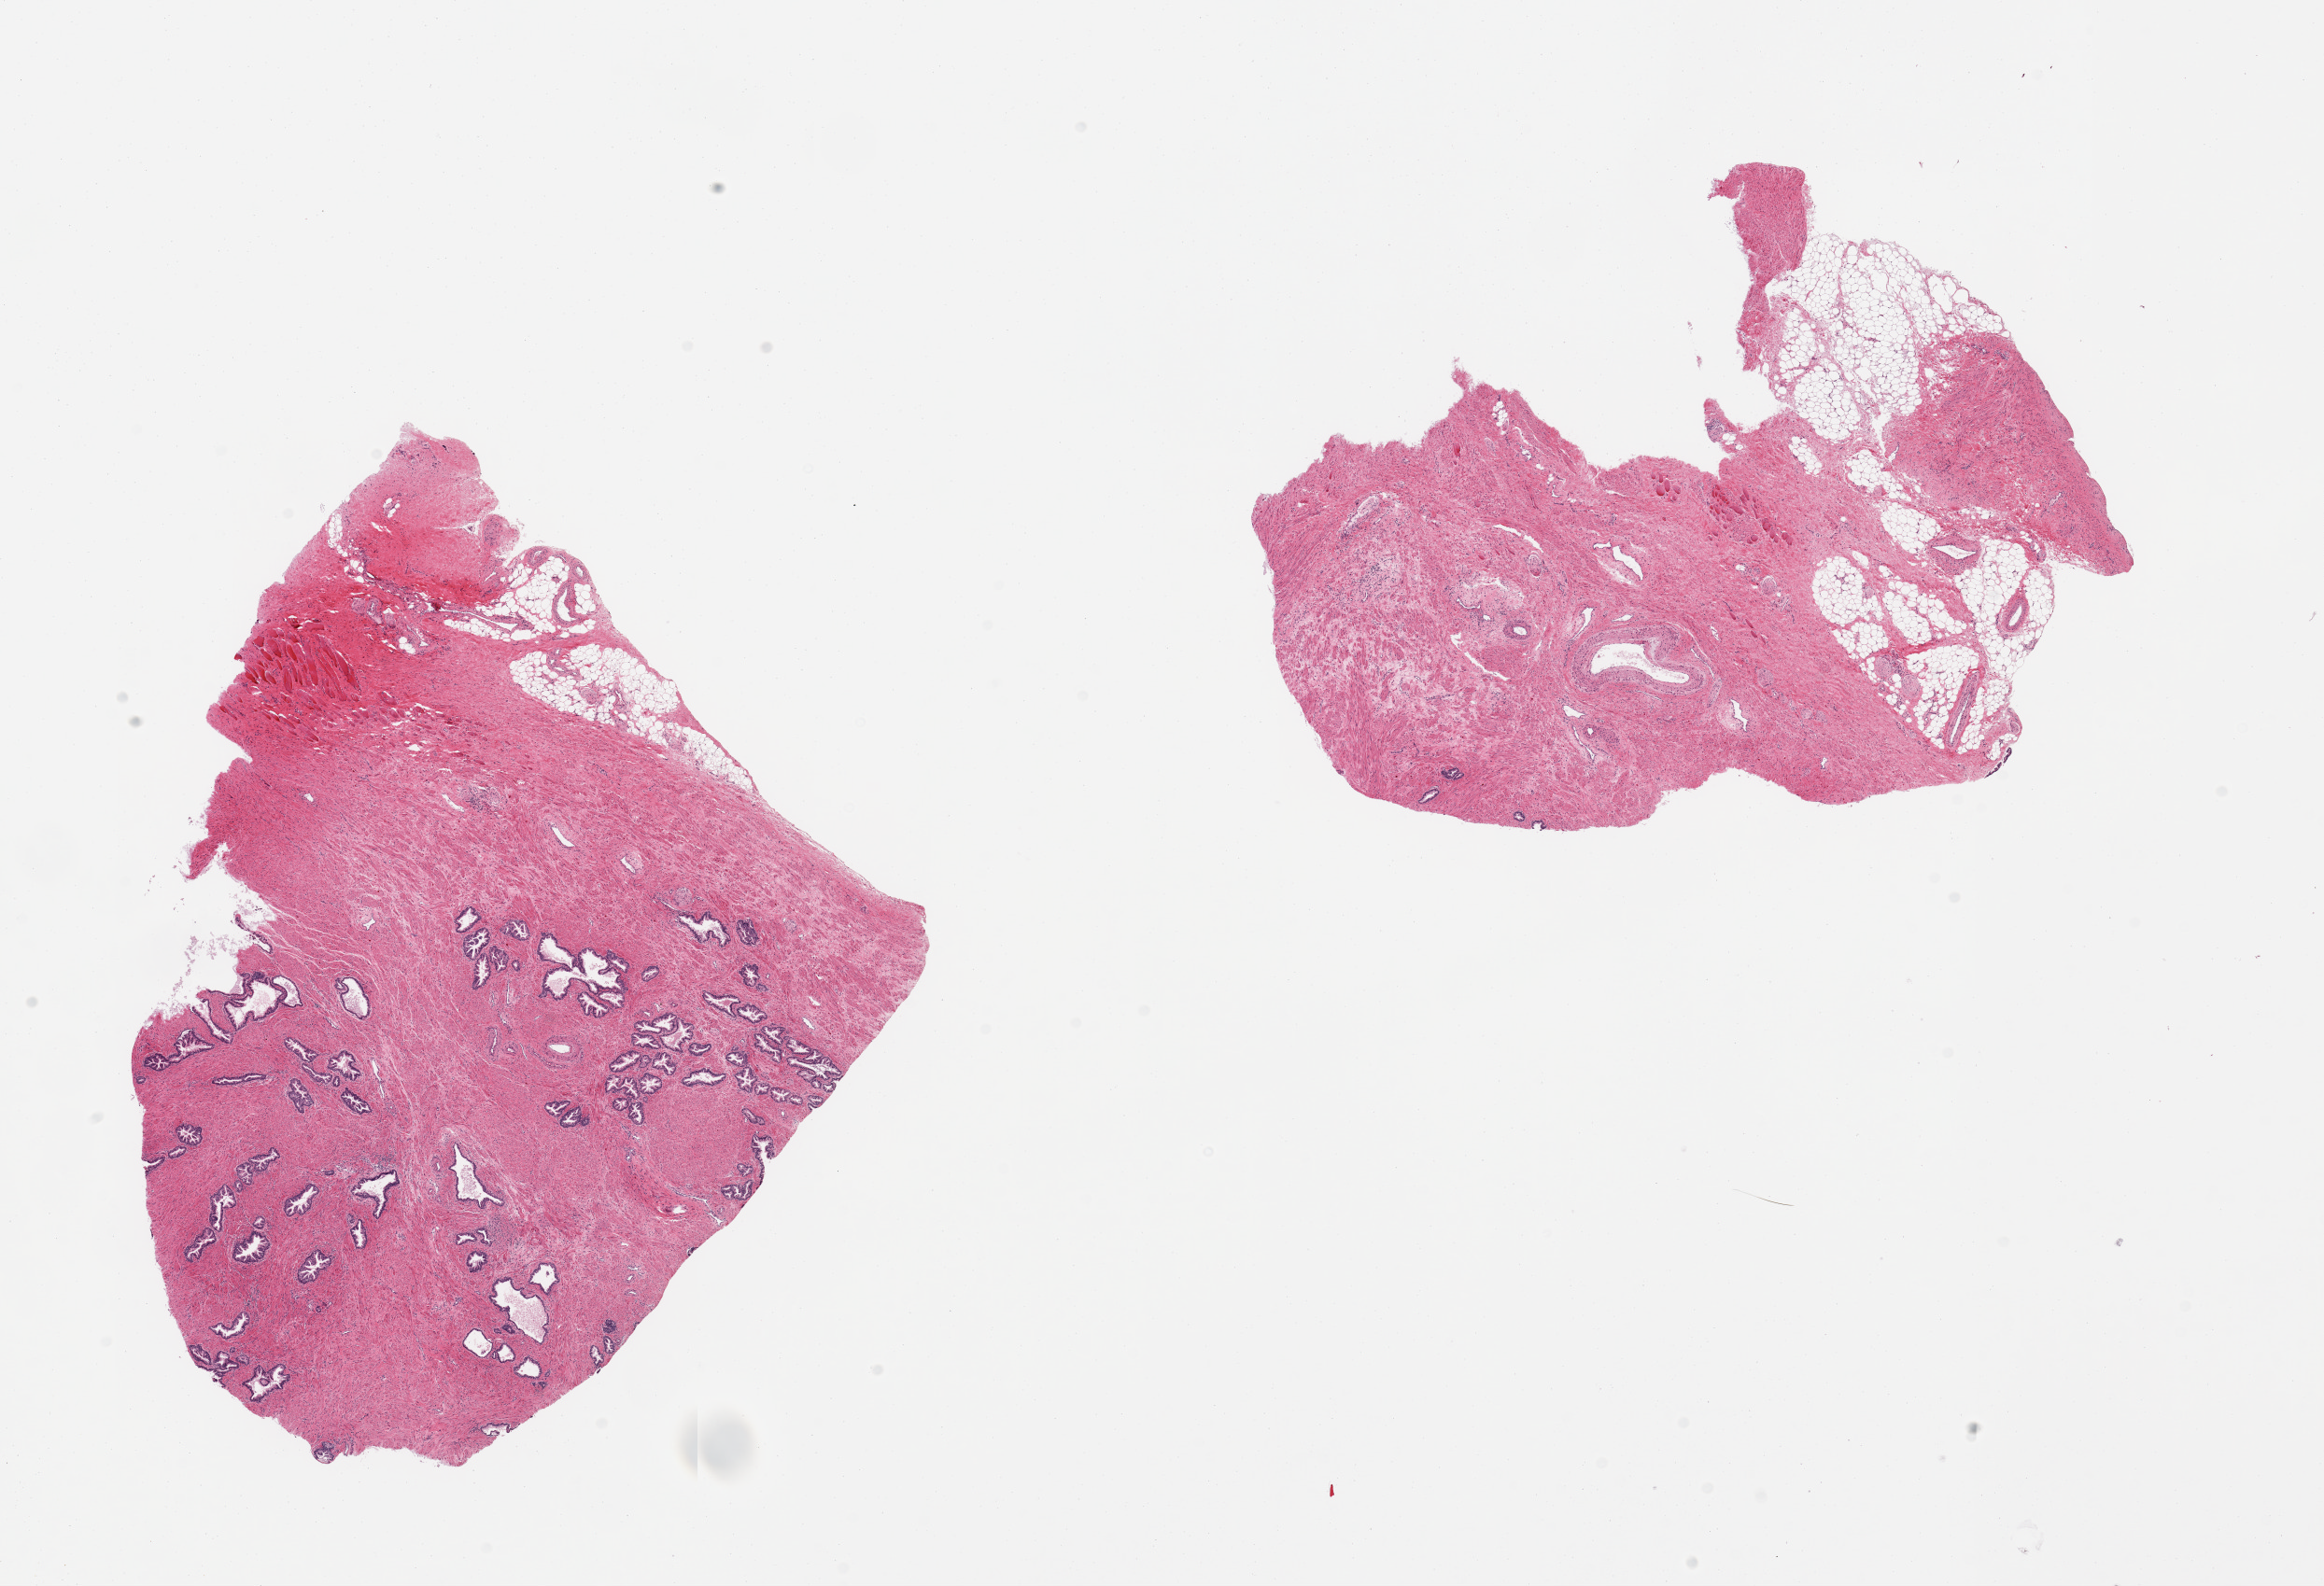
Whole-slide image, hematoxylin and eosin (H&E) stain, whole scanned area (about 19.7 x 13.4 mm, from a 20x scan) shown as a low-resolution overview; PAXgene-fixed paraffin-embedded (PFPE) section; sampled site (target tissue): prostate; donor tissue sample.
• pathologist's review note for this sample: 2 pieces, one contains well- preserved glands, the other is stroma and adherent fat